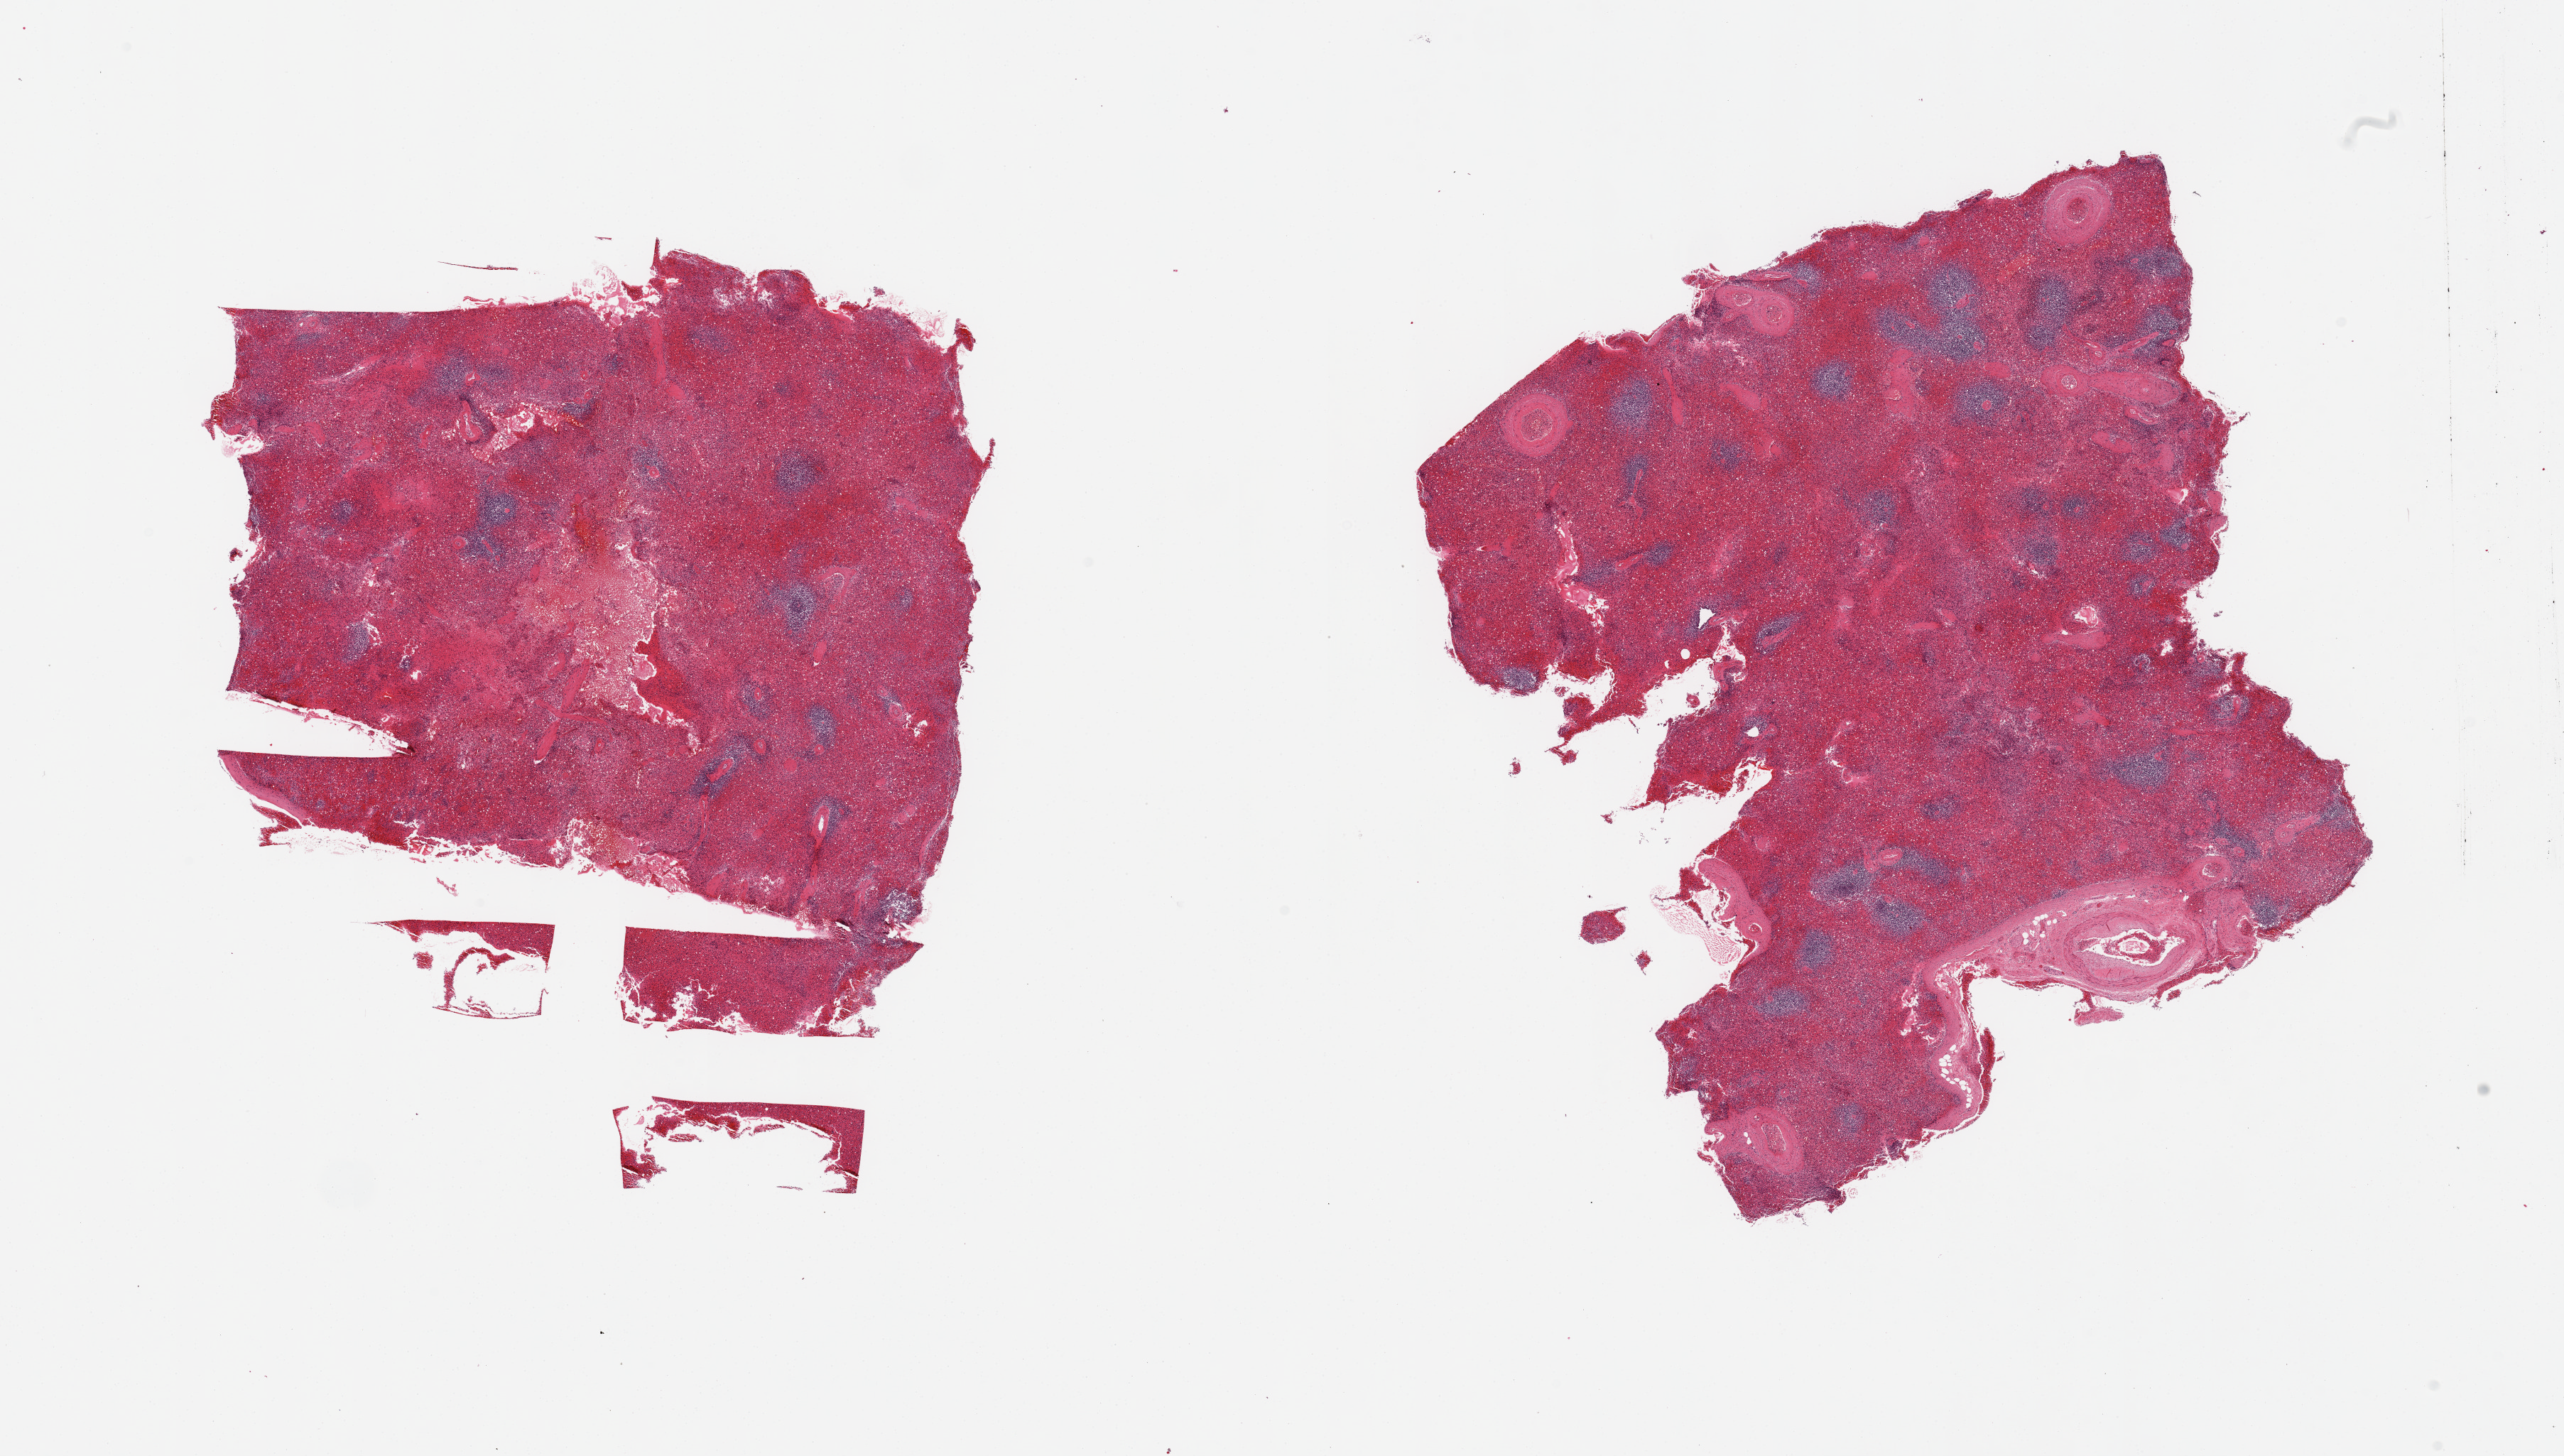
Digitized haematoxylin and eosin-stained section, low-resolution overview of the scanned area, about 28.5 x 16.2 mm (slide scanned at 20x), PAXgene-fixed, paraffin-embedded tissue, target tissue: spleen, tissue donor sample. Donor: male.
Pathologist's review note for this sample: 2 pieces; congestion, atherosclerosis of large vessel.